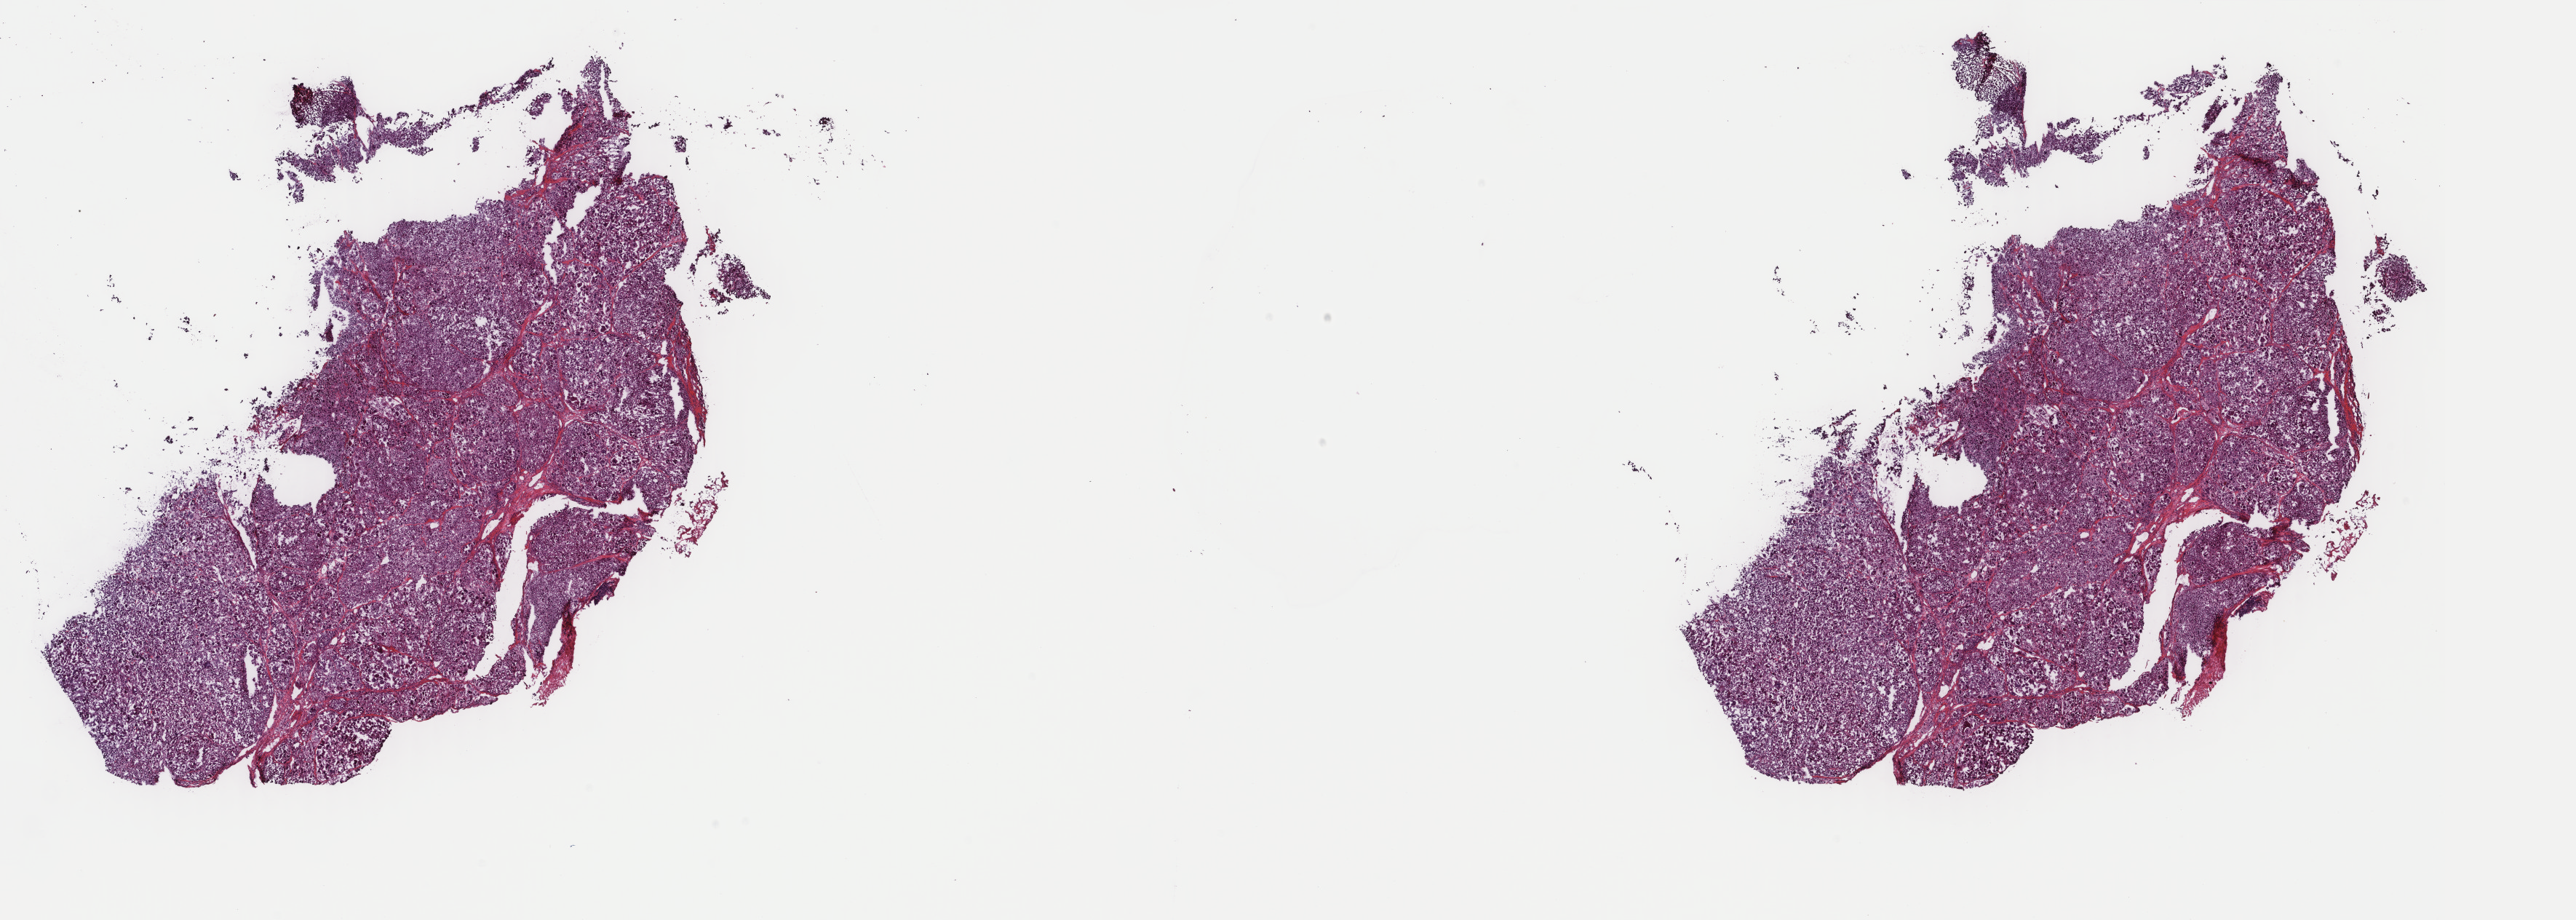
H&E whole-slide image — shown as a low-resolution overview of the whole scanned area (about 28.1 x 10.0 mm); frozen section from the top of the tissue portion; adrenal cortex, primary tumour sample. Patient: female, age at initial diagnosis 44 years. Composition of this section per pathologist review: tumour cells 90%, tumour nuclei 95%, normal cells 0%, stromal cells 5%, necrosis 5%. Inflammatory infiltration, as recorded: lymphocyte infiltration 0%, monocyte infiltration 0%, neutrophil infiltration 0%.
Lymph nodes positive (case pathology): 0 of 1 examined. Pathologic diagnosis: Adrenal cortical carcinoma (cortex of adrenal gland).